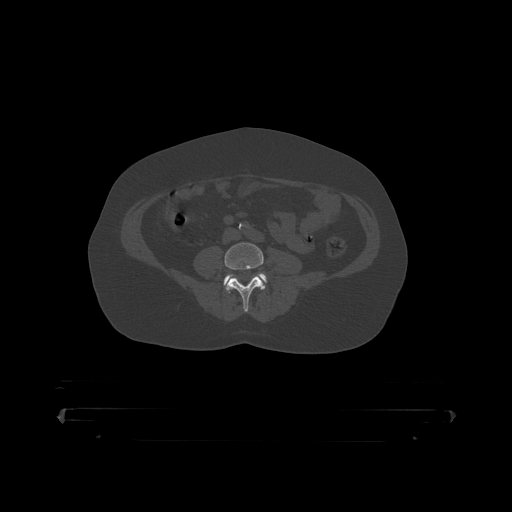
CT including the spine, one axial slice. Reconstruction kernel STANDARD. Bone window (W 1800 / L 400 HU). 1.25 mm slice thickness. 512 × 512 image matrix, field of view 650 × 650 mm. Patient: male, 60 years. From the clinical record (not read from this slice): primary cancer: prostate.
Annotated regions visible in this slice (semi-automatic segmentation, software-assisted and operator-edited):
- L4 vertebra: bounding box [x1, y1, x2, y2] px = [225, 243, 265, 313]
- L5 vertebra: [224, 275, 267, 285]